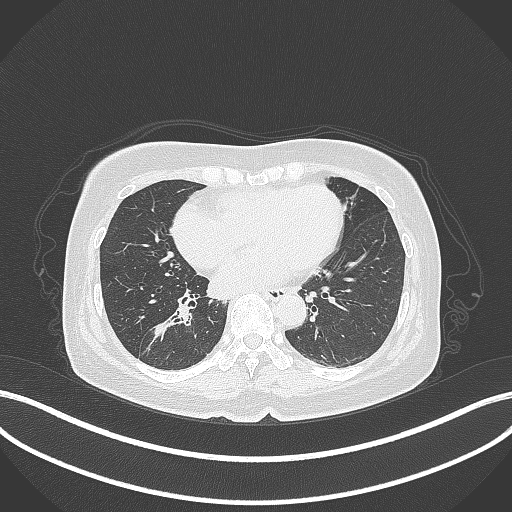
Chest CT, one axial slice; position 162 of 429 along the scan axis; reconstruction kernel B70f; lung window (W 1500 / L -600 HU); 1 mm slice thickness; 512 × 512 image matrix, field of view 400 × 400 mm. Patient: female, 67 years. Case-level facts recorded for this patient, not image findings: clinical TNM (as recorded): T1c N1 M0.
Annotated regions visible in this slice (bounding box drawn by a radiologist):
- lung tumour (recorded histology: adenocarcinoma): box from (x=146, y=302) to (x=196, y=357) px